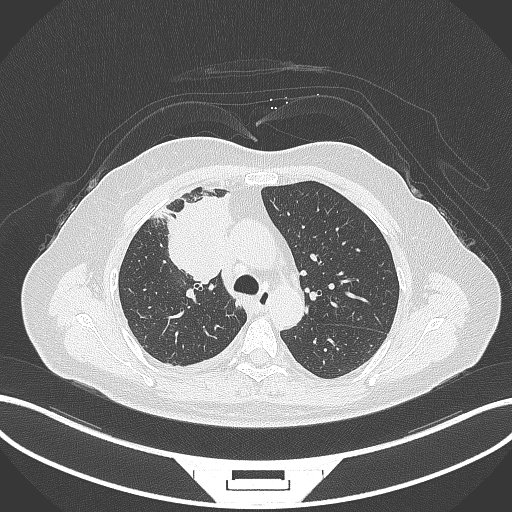
Chest CT, one axial slice. Slice 197 of 305 in the series (ordered by position). Lung window (W 1500 / L -600 HU). 1 mm slice thickness. 512 × 512 image matrix. Female patient, age 52 years. Case-level facts recorded for this patient, not image findings: clinical TNM (as recorded): T3 N1 M1.
Outlined on this slice (bounding box drawn by a radiologist):
- lung tumour (recorded histology: adenocarcinoma): bounding box (x1, y1, x2, y2) in pixels: (149, 191, 233, 287)